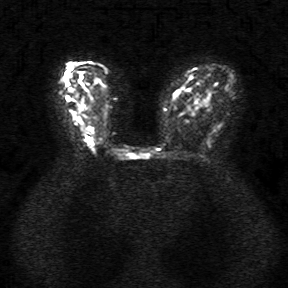
Breast MRI, one axial slice; position 18 of 34 along the scan axis; diffusion-weighted series; image 2 of 4 stored at this slice position (different b-values; order by instance number); 1.5 T; 288 × 288 image matrix, field of view 340 × 340 mm. Female patient.
Annotated regions visible in this slice (outlined manually by an expert reader):
- tumour on diffusion-weighted imaging: bounding box (x1, y1, x2, y2) in pixels: (67, 96, 85, 110)